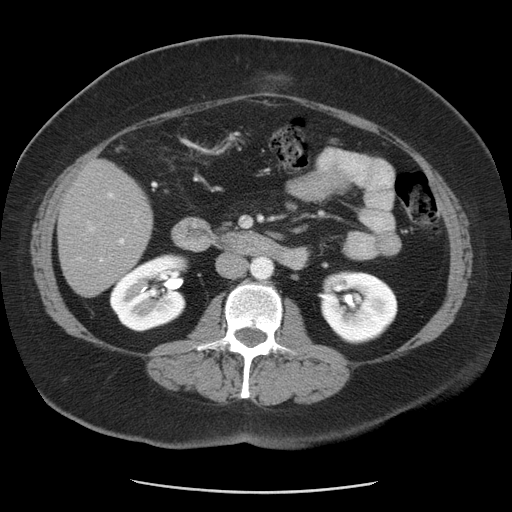
Contrast-enhanced abdominal CT, one axial slice; slice 15 of 55 in the series (ordered by position); reconstruction kernel STANDARD; 120 kVp; intravenous contrast given; soft-tissue window (W 400 / L 40 HU); 512 × 512 image matrix. Female patient, age 52 years. From the clinical record (not read from this slice): diagnosis: colorectal cancer liver metastases, imaged before liver resection; multiple liver metastases: yes; largest metastasis: 2.5 cm.
Structures marked on this image (outlined manually by an expert reader):
- liver: bounding box <59,160,152,297> (left, top, right, bottom; pixels)
- planned liver remnant (the part of the liver to remain after resection): <58,191,140,297>
- portal vein (with intrahepatic branches): <77,191,138,264>